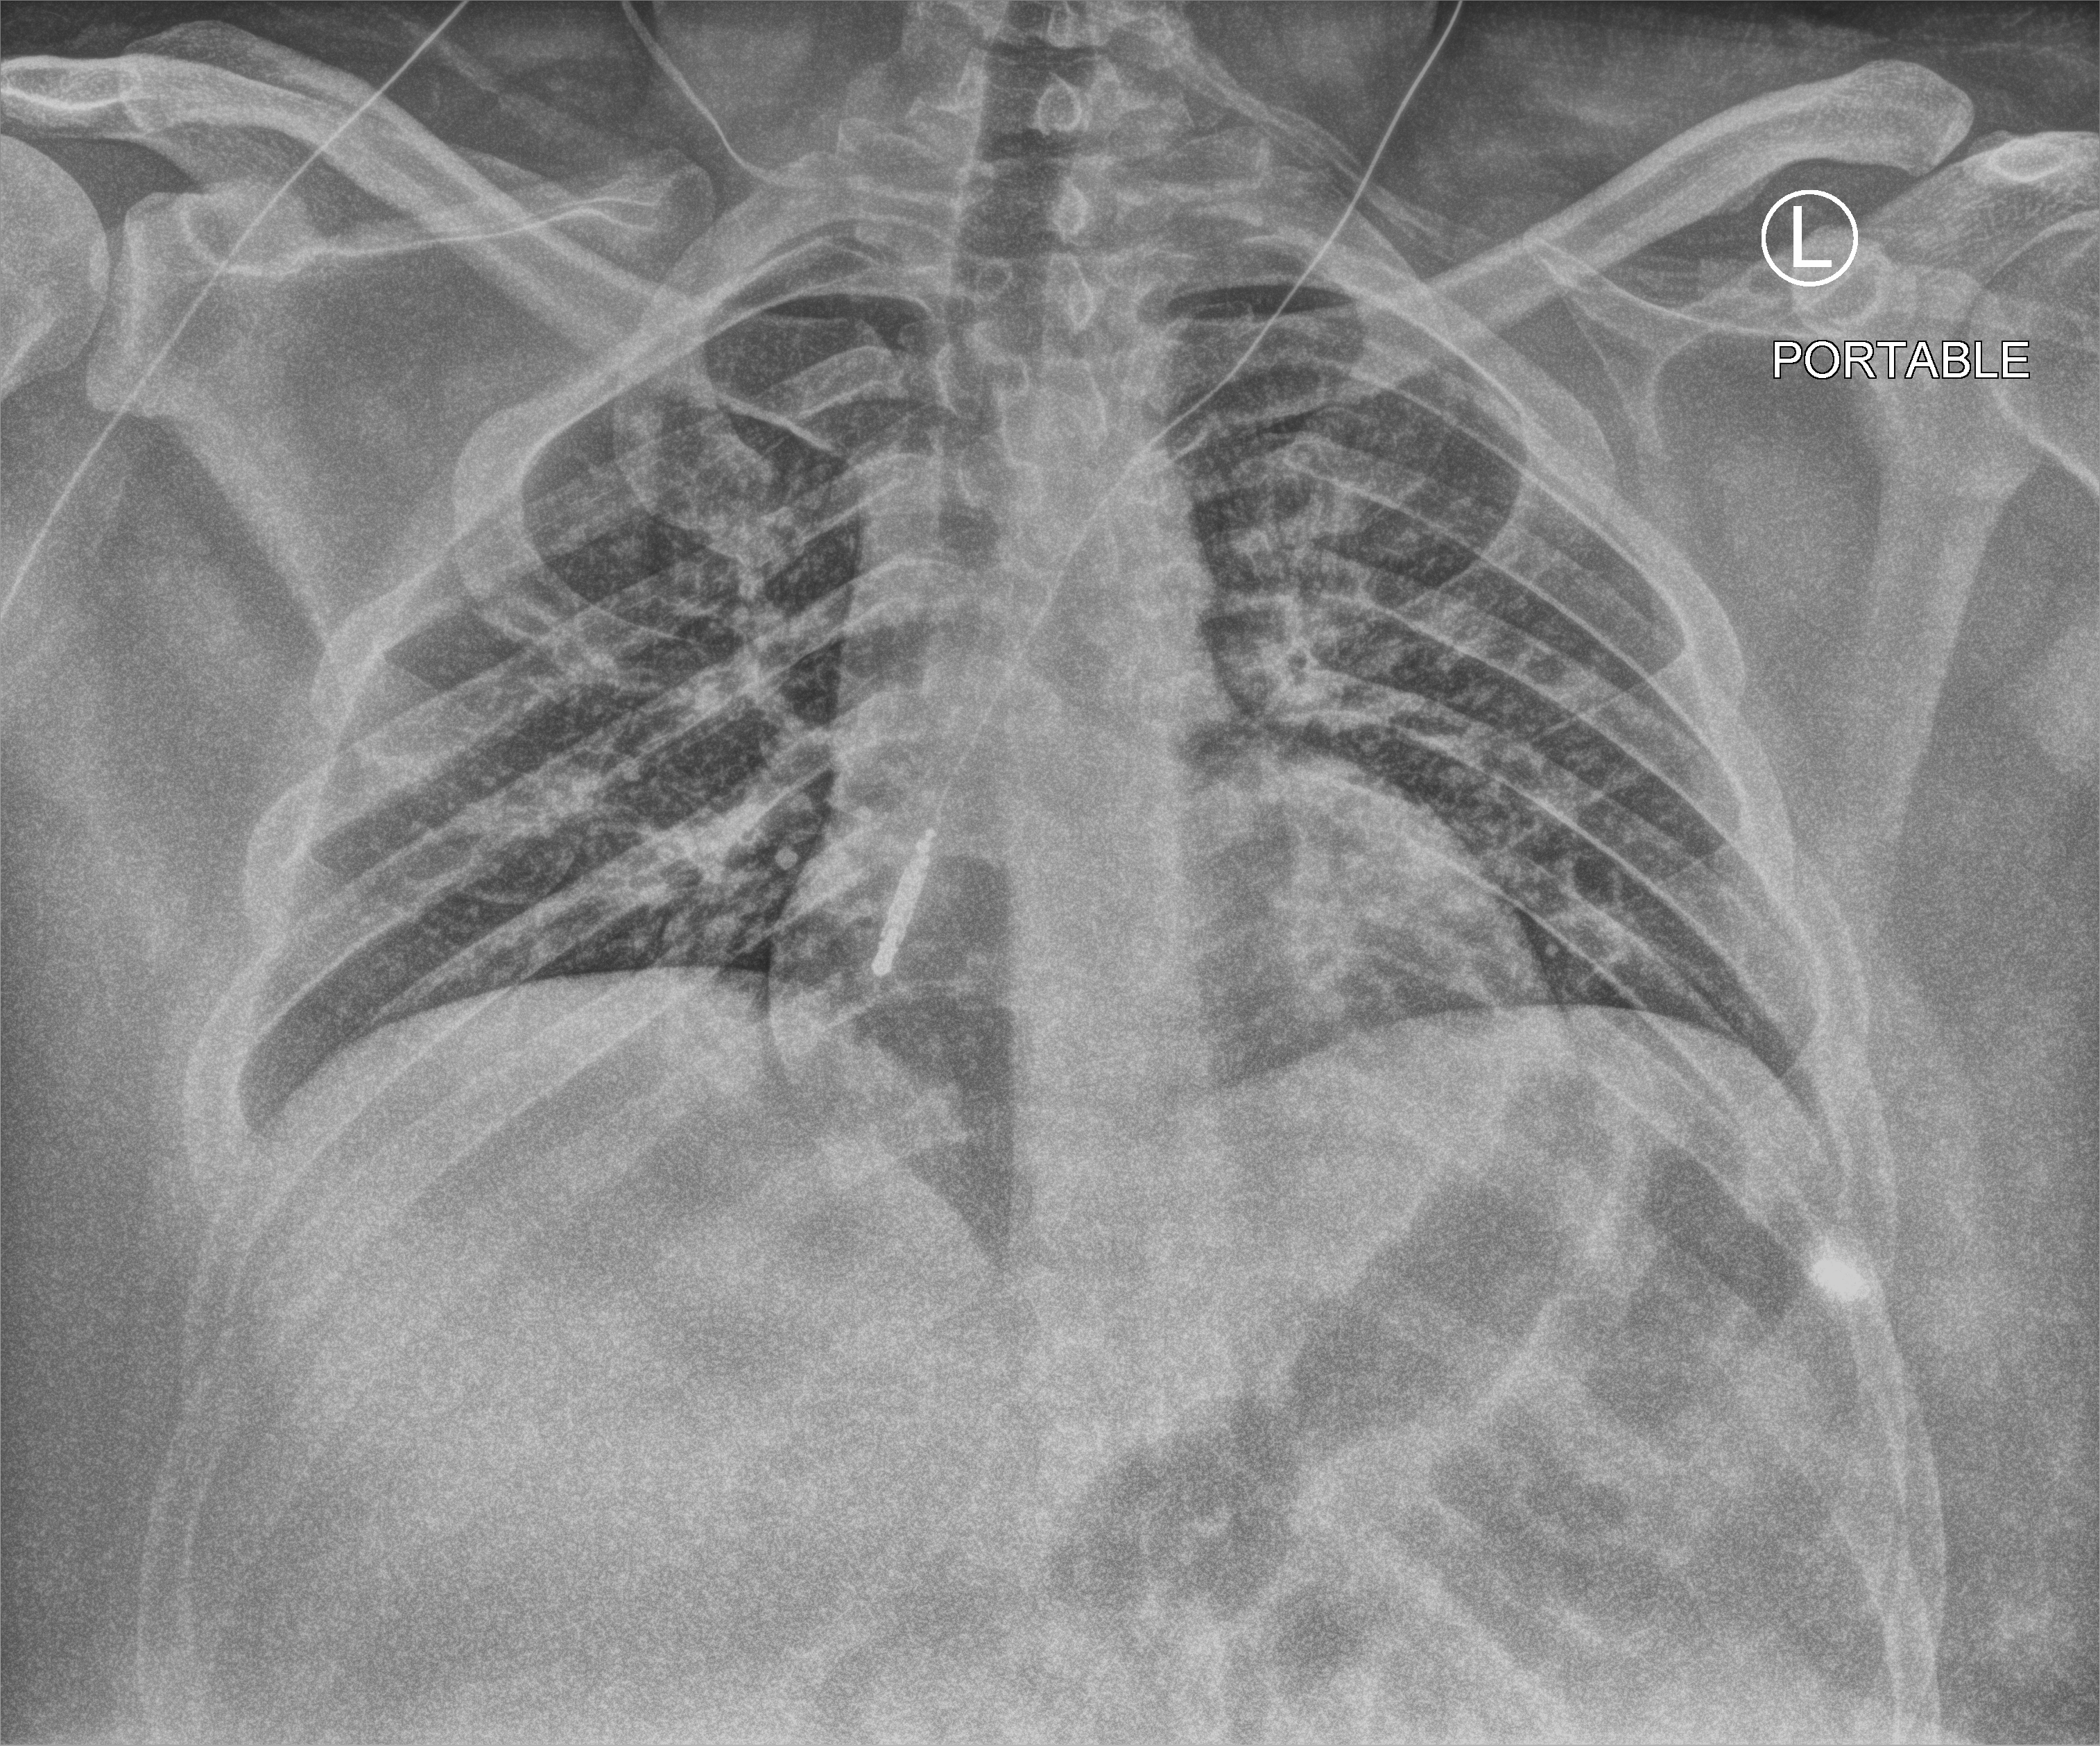
Portable chest radiograph; anteroposterior (AP) projection. Male patient hospitalised with COVID-19, age 18–59 years.
Hospital-stay facts (about this admission, not read from this image; timing relative to this image not recorded): hypertension (admission record): no; admitted to intensive care during this hospital stay: no.